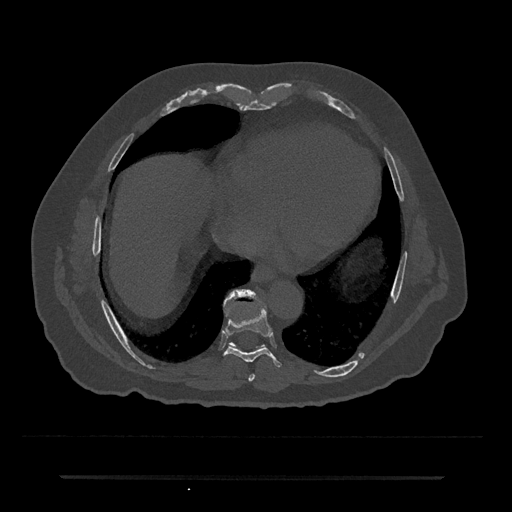
CT including the spine, one axial slice. Reconstruction kernel Br40s/3. 120 kVp. Bone window (W 1800 / L 400 HU). 0.5 mm slice thickness. 512 × 512 image matrix, field of view 437 × 437 mm. Patient: male, 69 years. Case-level facts recorded for this patient, not image findings: primary cancer: prostate.
Structures marked on this image (semi-automatically segmented with operator editing):
- T7 vertebra: box from (x=248, y=374) to (x=255, y=381) px
- T8 vertebra: (x=224, y=305)–(x=282, y=367)
- T9 vertebra: (x=227, y=289)–(x=255, y=301)